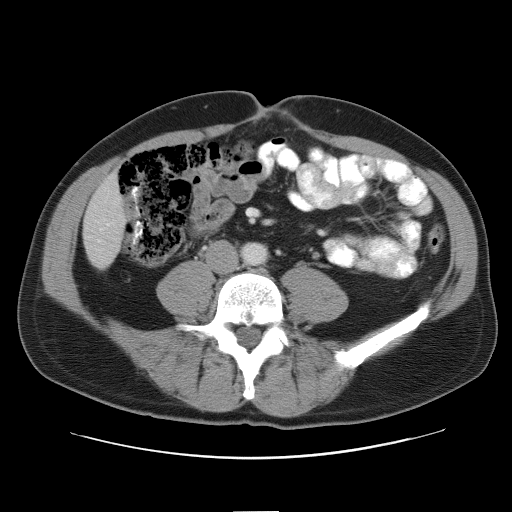
Contrast-enhanced abdominal CT, one axial slice. Reconstruction kernel STANDARD. Intravenous contrast given. Soft-tissue window (W 400 / L 40 HU). 5 mm slice thickness. 512 × 512 image matrix. Male patient, age 70 years. Case-level facts recorded for this patient, not image findings: diagnosis: colorectal cancer liver metastases, imaged before liver resection; multiple liver metastases: yes; largest metastasis: 4 cm; disease in both lobes: yes.
Outlined on this slice (expert manual segmentation):
- liver: bounding box <84,176,125,268> (left, top, right, bottom; pixels)